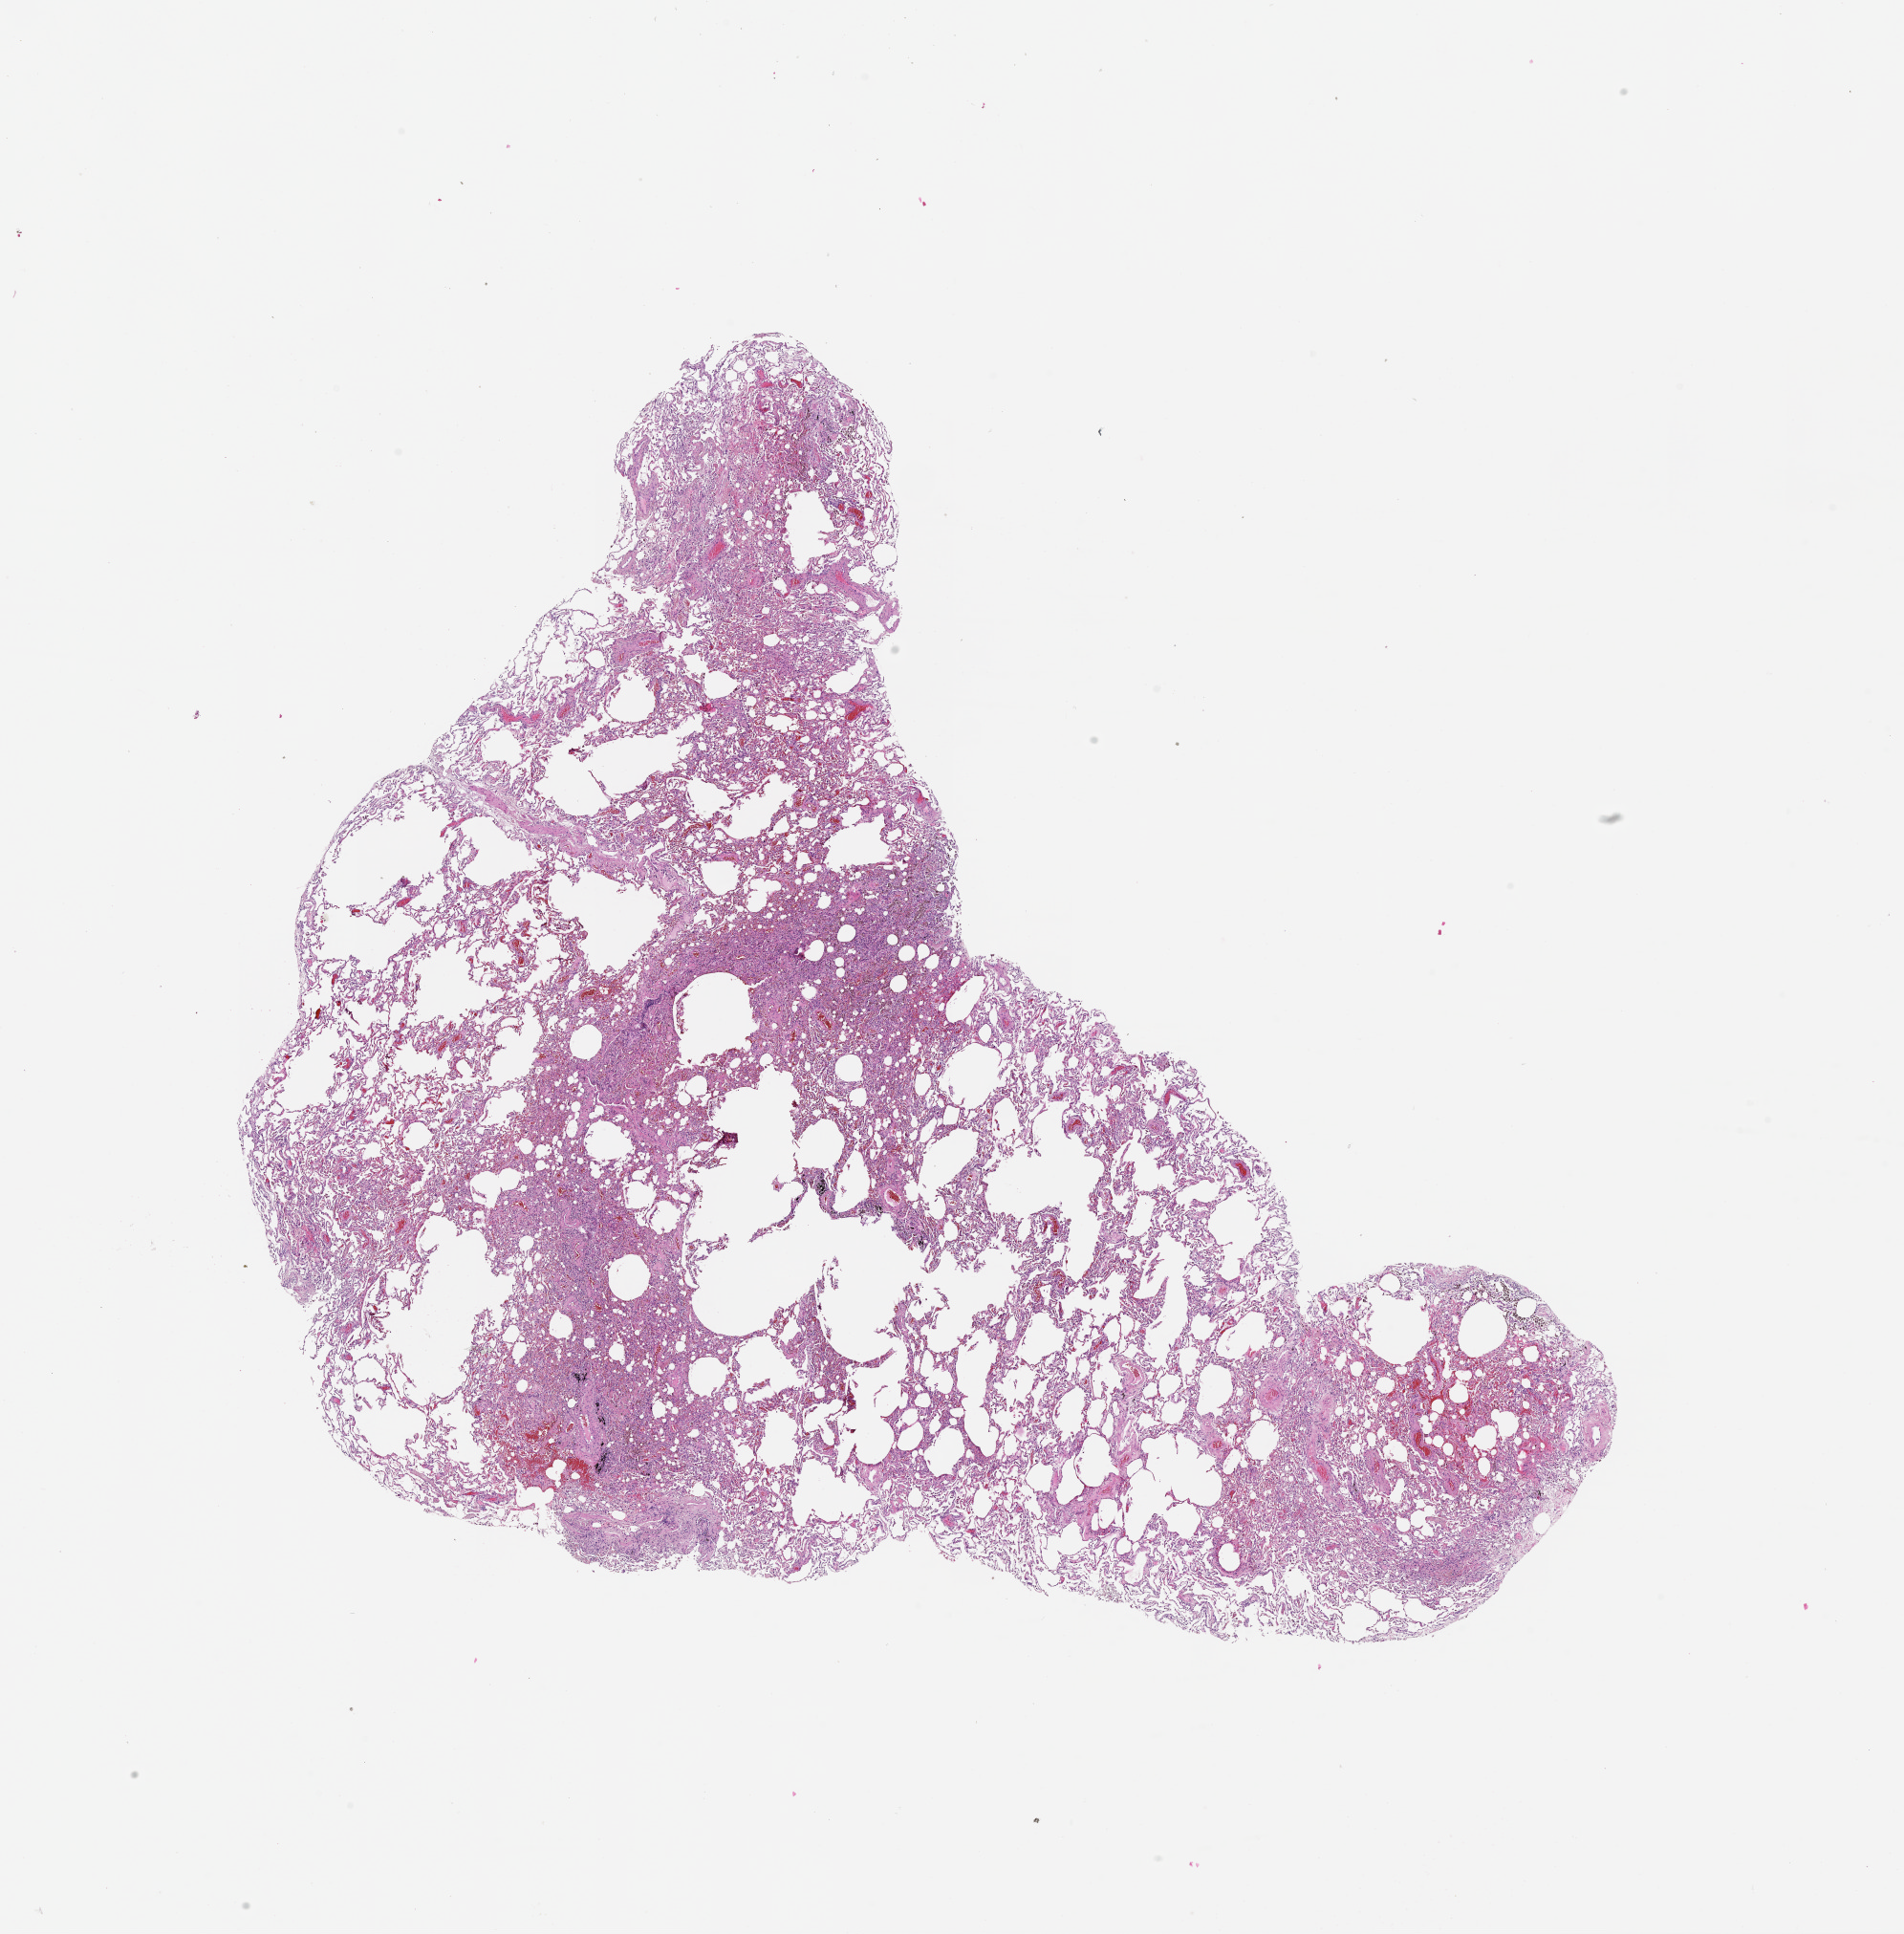
Whole-slide histology image, H&E, whole scanned area (about 16.0 x 16.3 mm, acquisition: 20x scan) shown as a low-resolution overview; lung, normal (non-tumour) tissue. Patient: male, age 60 years.
* this section: normal (non-tumour) tissue from the same patient
* patient diagnosis (cohort enrolment): squamous cell carcinoma (lung)